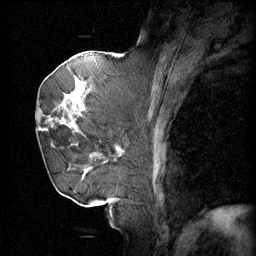
Breast MRI (dynamic contrast-enhanced), one sagittal slice; position 27 of 60 along the scan axis; 4 images stored at this slice position (order not interpretable as contrast timing); 1.5 T; TE 4.2 ms, TR 11 ms; 256 × 256 image matrix, field of view 220 × 220 mm. Patient: female, 72 years.
Annotated regions visible in this slice (semi-automatically segmented with operator editing):
- analysis volume of interest (the breast-tissue region the enhancement analysis was run in; not a lesion): bounding box (x1, y1, x2, y2) in pixels: (43, 68, 109, 163)
- tumour enhancement mask (voxels above the 70 % enhancement threshold inside the analysis volume of interest): (43, 74, 109, 163)